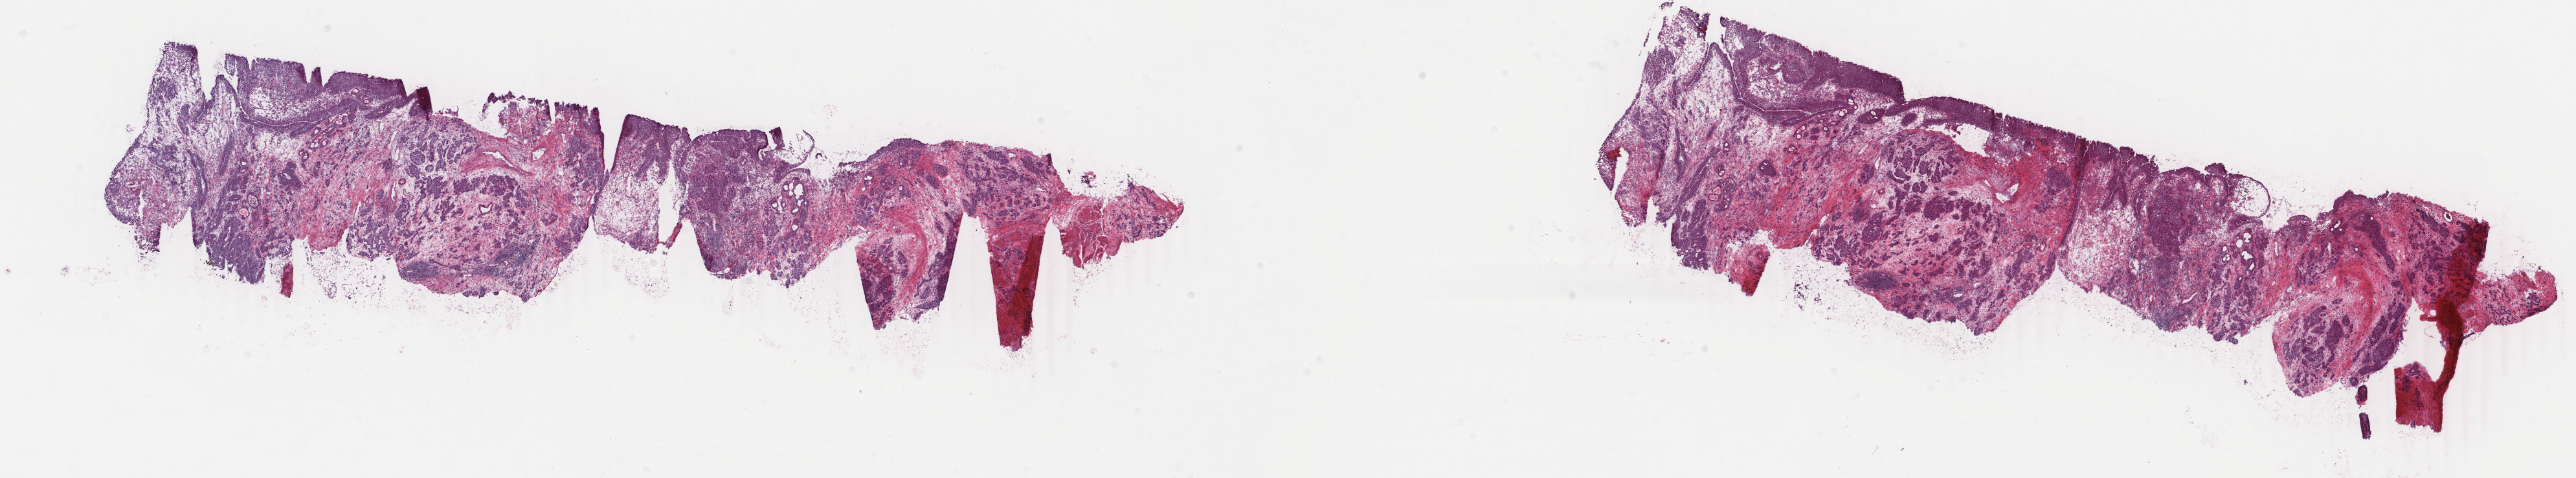
H&E whole-slide image, shown as a low-resolution overview of the whole scanned area (about 31.6 x 5.9 mm, from a 40x scan); frozen section from the bottom of the tissue portion; bladder, primary tumour sample. Male patient; age at initial diagnosis 84 years. Histologic grade: high grade. Composition of this section per pathologist review: tumour cells 60%, tumour nuclei 60%, normal cells 8%, stromal cells 32%, necrosis 0%. Inflammatory infiltration, as recorded: lymphocyte infiltration 2%, monocyte infiltration 0%, neutrophil infiltration 0%.
TNM: T3a N2 MX. Diagnosis: Papillary transitional cell carcinoma. AJCC pathologic stage: IV. Lymph nodes positive (case pathology): 8 of 13 examined.